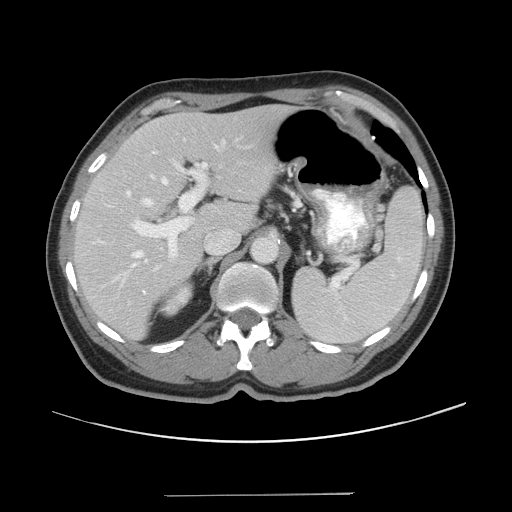
Contrast-enhanced abdominal CT, one axial slice. Slice 27 of 43 in the series (ordered by position). Reconstruction kernel STANDARD. 120 kVp. Intravenous contrast given. Soft-tissue window (W 400 / L 40 HU). 512 × 512 image matrix. Male patient, age 65 years. From the clinical record (not read from this slice): diagnosis: colorectal cancer liver metastases, imaged before liver resection; multiple liver metastases: no; largest metastasis: 3.8 cm; chemotherapy before resection: yes.
Structures marked on this image (expert manual segmentation):
- hepatic veins: box from (x=113, y=174) to (x=169, y=287) px
- liver: (x=75, y=107)–(x=281, y=338)
- planned liver remnant (the part of the liver to remain after resection): (x=75, y=107)–(x=281, y=338)
- portal vein (with intrahepatic branches): (x=126, y=138)–(x=267, y=271)